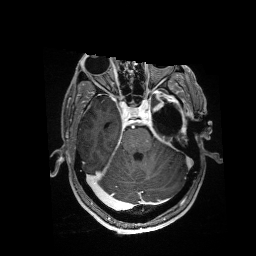
Brain MRI from a brain-tumour surgery series, one axial slice; slice 111 of 176 in the series (ordered by position); T1-weighted post-contrast; 1 mm slice thickness; 256 × 256 image matrix, field of view 256 × 256 mm. From the clinical record (not read from this slice): histopathology: Glioblastoma; WHO grade: 4; IDH mutation: no; tumour location: Left Anterior/Superior Temporal.
Structures marked on this image (expert manual segmentation):
- residual tumour: box from (x=154, y=90) to (x=183, y=114) px